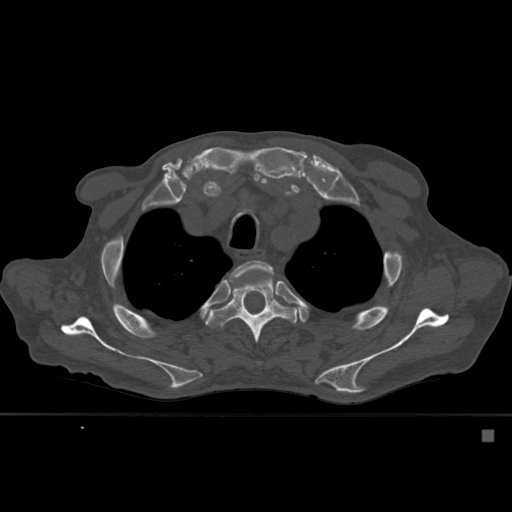
CT including the spine, one axial slice. Position 420 of 527 along the scan axis. Bone window (W 1800 / L 400 HU). 1.5 mm slice thickness. 512 × 512 image matrix, field of view 373 × 373 mm. Male patient, age 78 years. From the clinical record (not read from this slice): primary cancer: prostate.
Outlined on this slice (semi-automatically segmented with operator editing):
- T3 vertebra: bounding box <229,260,277,289> (left, top, right, bottom; pixels)
- T4 vertebra: <204,273,298,366>